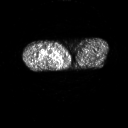
FDG PET of an extremity soft-tissue mass (from a PET/CT study), one axial slice. Position 239 of 311 along the scan axis. 3.27 mm slice thickness. 128 × 128 image matrix. Male patient, age 50 years. Case-level facts recorded for this patient, not image findings: histological type: undifferentiated - pleiomorphic; grade: high; site of the primary tumour: right thigh.
Structures marked on this image (expert contour drawn on MRI and transferred to this co-registered scan by the dataset authors):
- gross tumour volume including surrounding oedema: bounding box (x1, y1, x2, y2) in pixels: (41, 50, 56, 60)